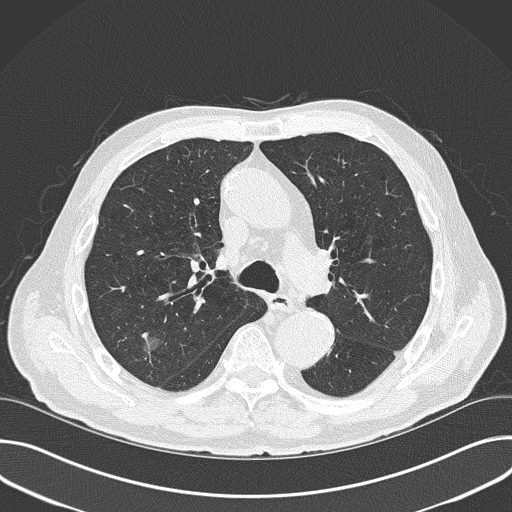
Low-dose screening chest CT, one axial slice; slice 108 of 177 in the series (ordered by position); reconstruction kernel B50f; 120 kVp; lung window (W 1500 / L -600 HU); 2 mm slice thickness; 512 × 512 image matrix.
Structures marked on this image (manually delineated by an expert):
- lesion 1 (tumor, upper lobe of right lung): box from (x=148, y=336) to (x=162, y=351) px